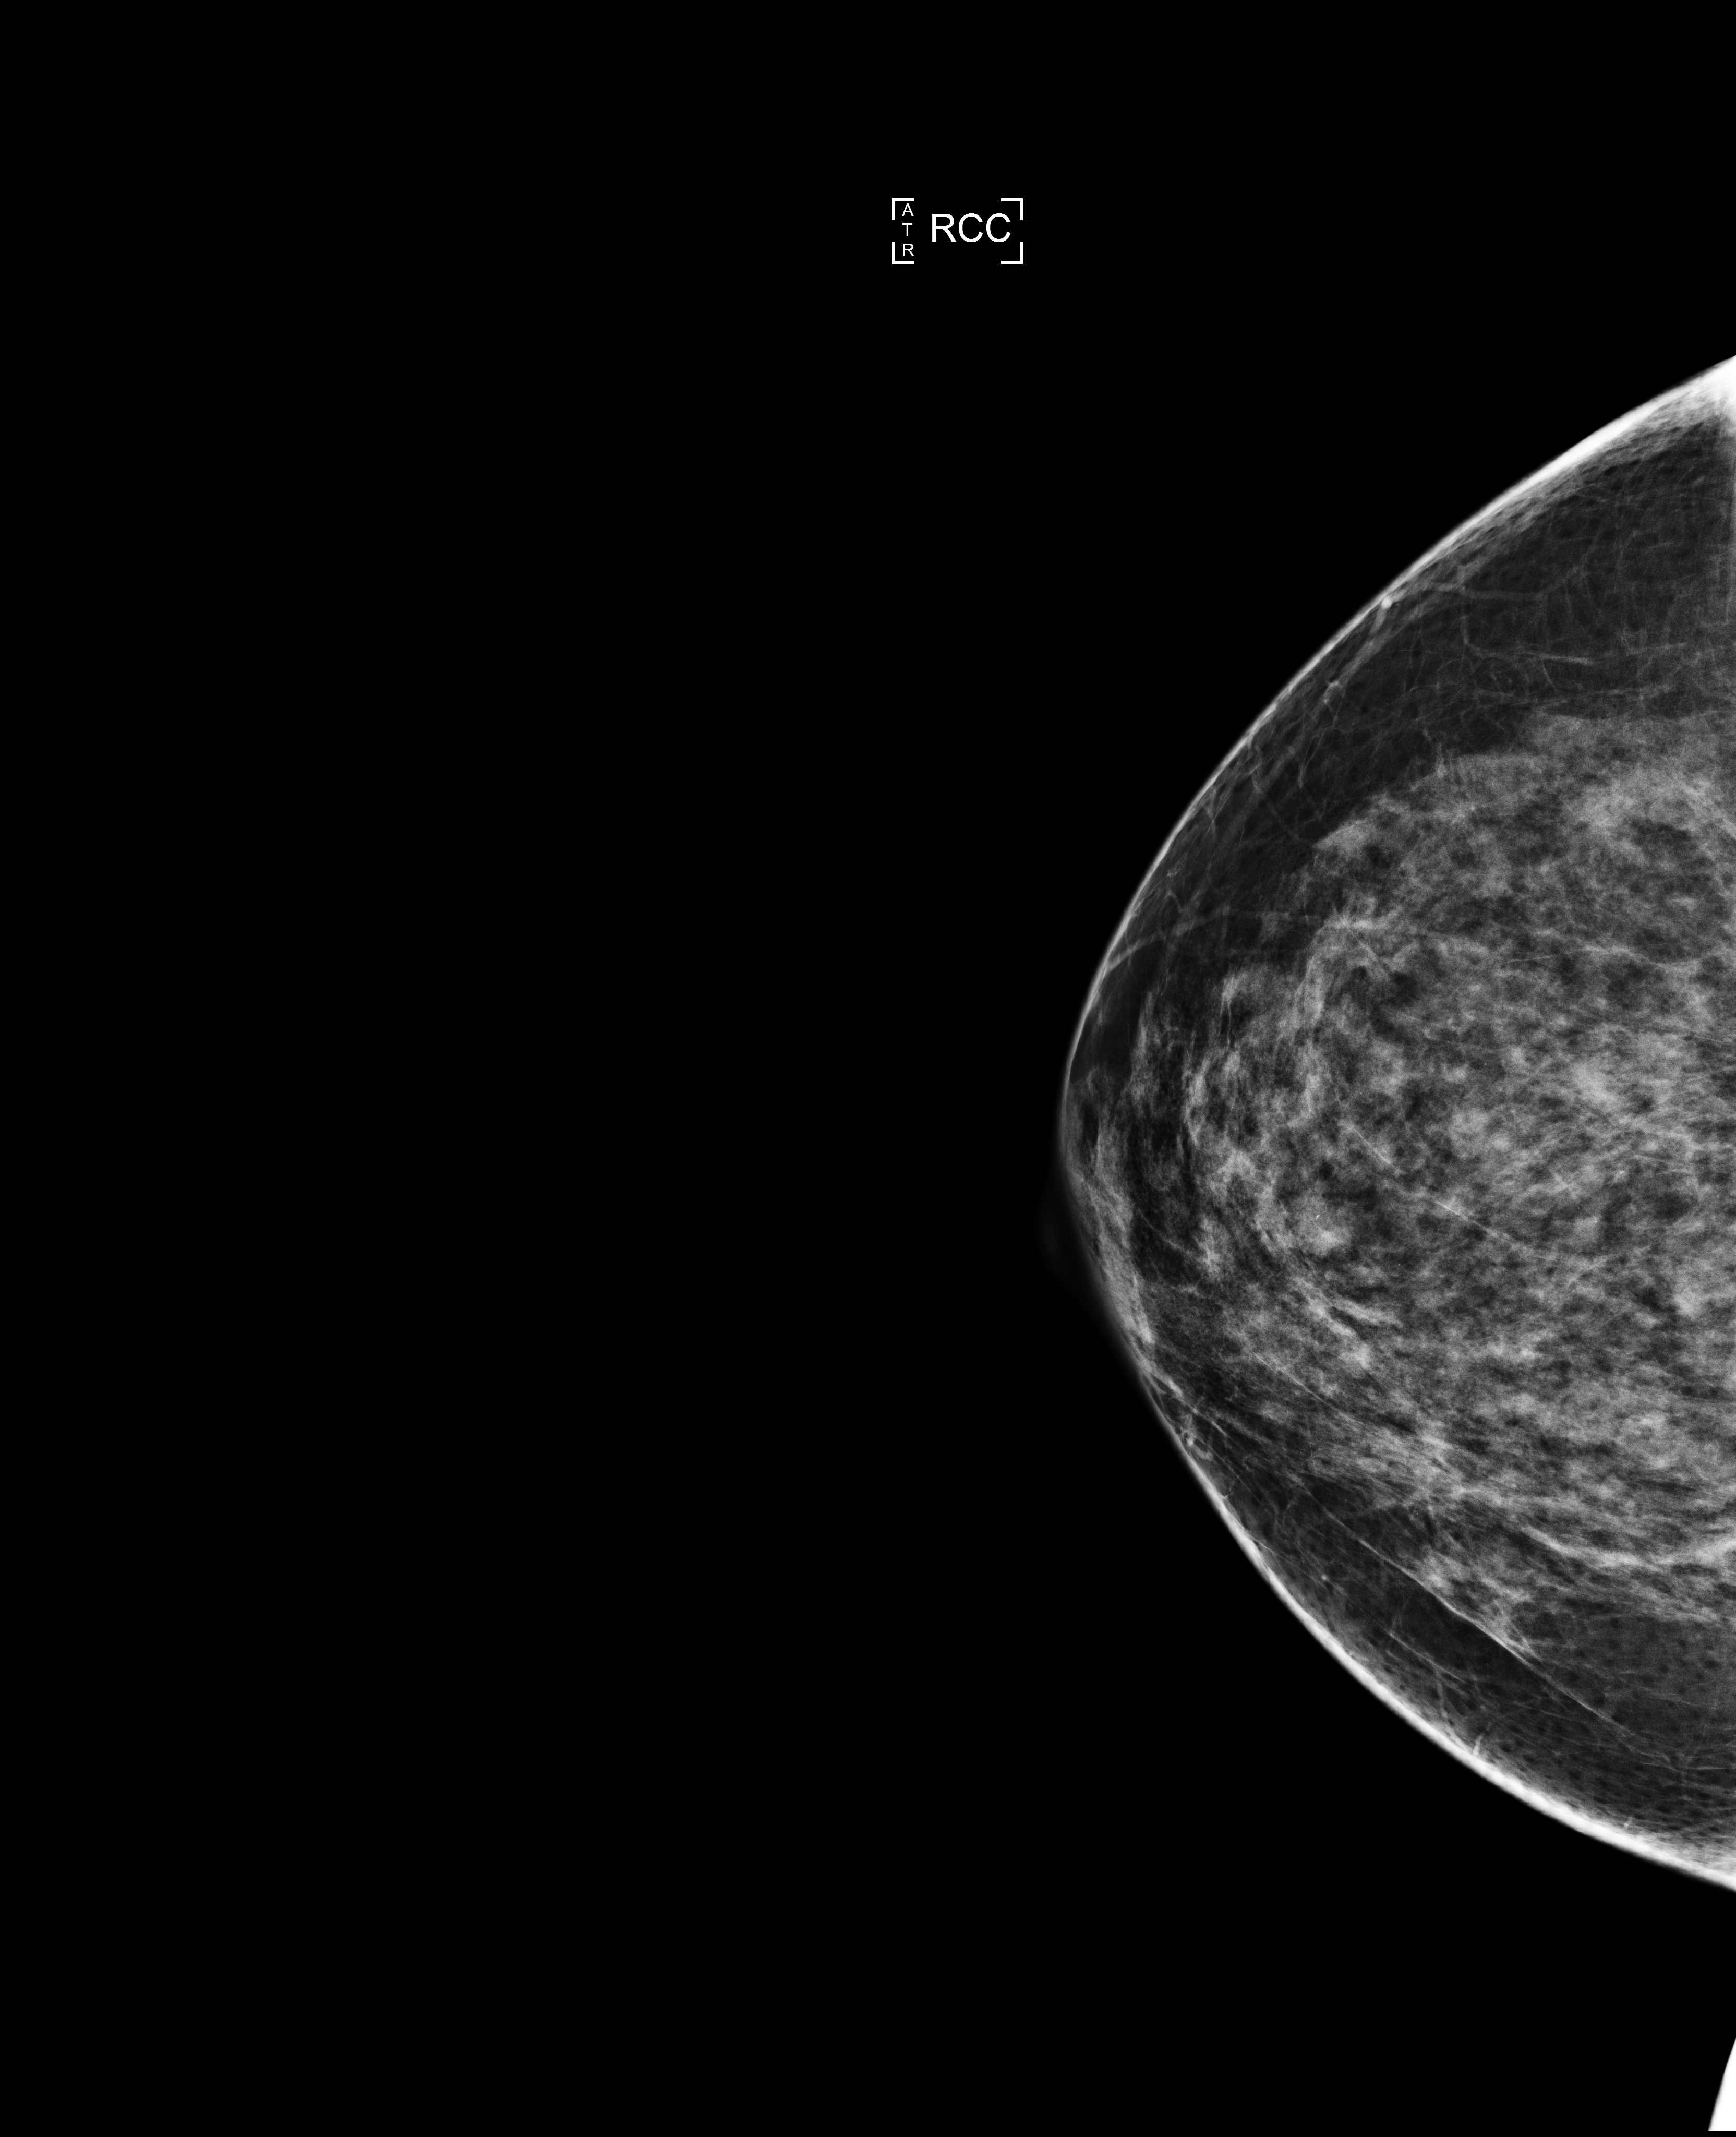
Annual screening mammography examination, compressed breast thickness 68 mm, system: Selenia Dimensions. Patient aged 53 years (female).
Image type: full-field digital mammogram. Breast: right. Projection: cranio-caudal projection.